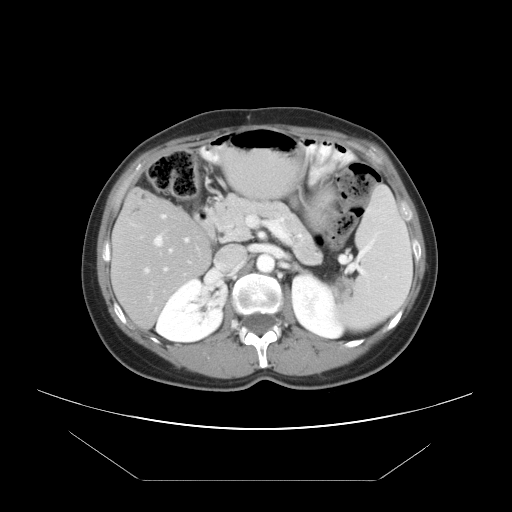
Contrast-enhanced abdominal CT, one axial slice. Position 22 of 45 along the scan axis. Reconstruction kernel STANDARD. Soft-tissue window (W 400 / L 40 HU). 5 mm slice thickness. 512 × 512 image matrix, field of view 405 × 405 mm. Female patient, age 52 years. Case-level facts recorded for this patient, not image findings: diagnosis: colorectal cancer liver metastases, imaged before liver resection; multiple liver metastases: yes; largest metastasis: 2.5 cm; chemotherapy before resection: yes.
Structures marked on this image (expert manual segmentation):
- hepatic veins: box from (x=145, y=236) to (x=167, y=272) px
- liver: (x=113, y=190)–(x=209, y=327)
- planned liver remnant (the part of the liver to remain after resection): (x=113, y=190)–(x=208, y=327)
- portal vein (with intrahepatic branches): (x=141, y=214)–(x=190, y=253)